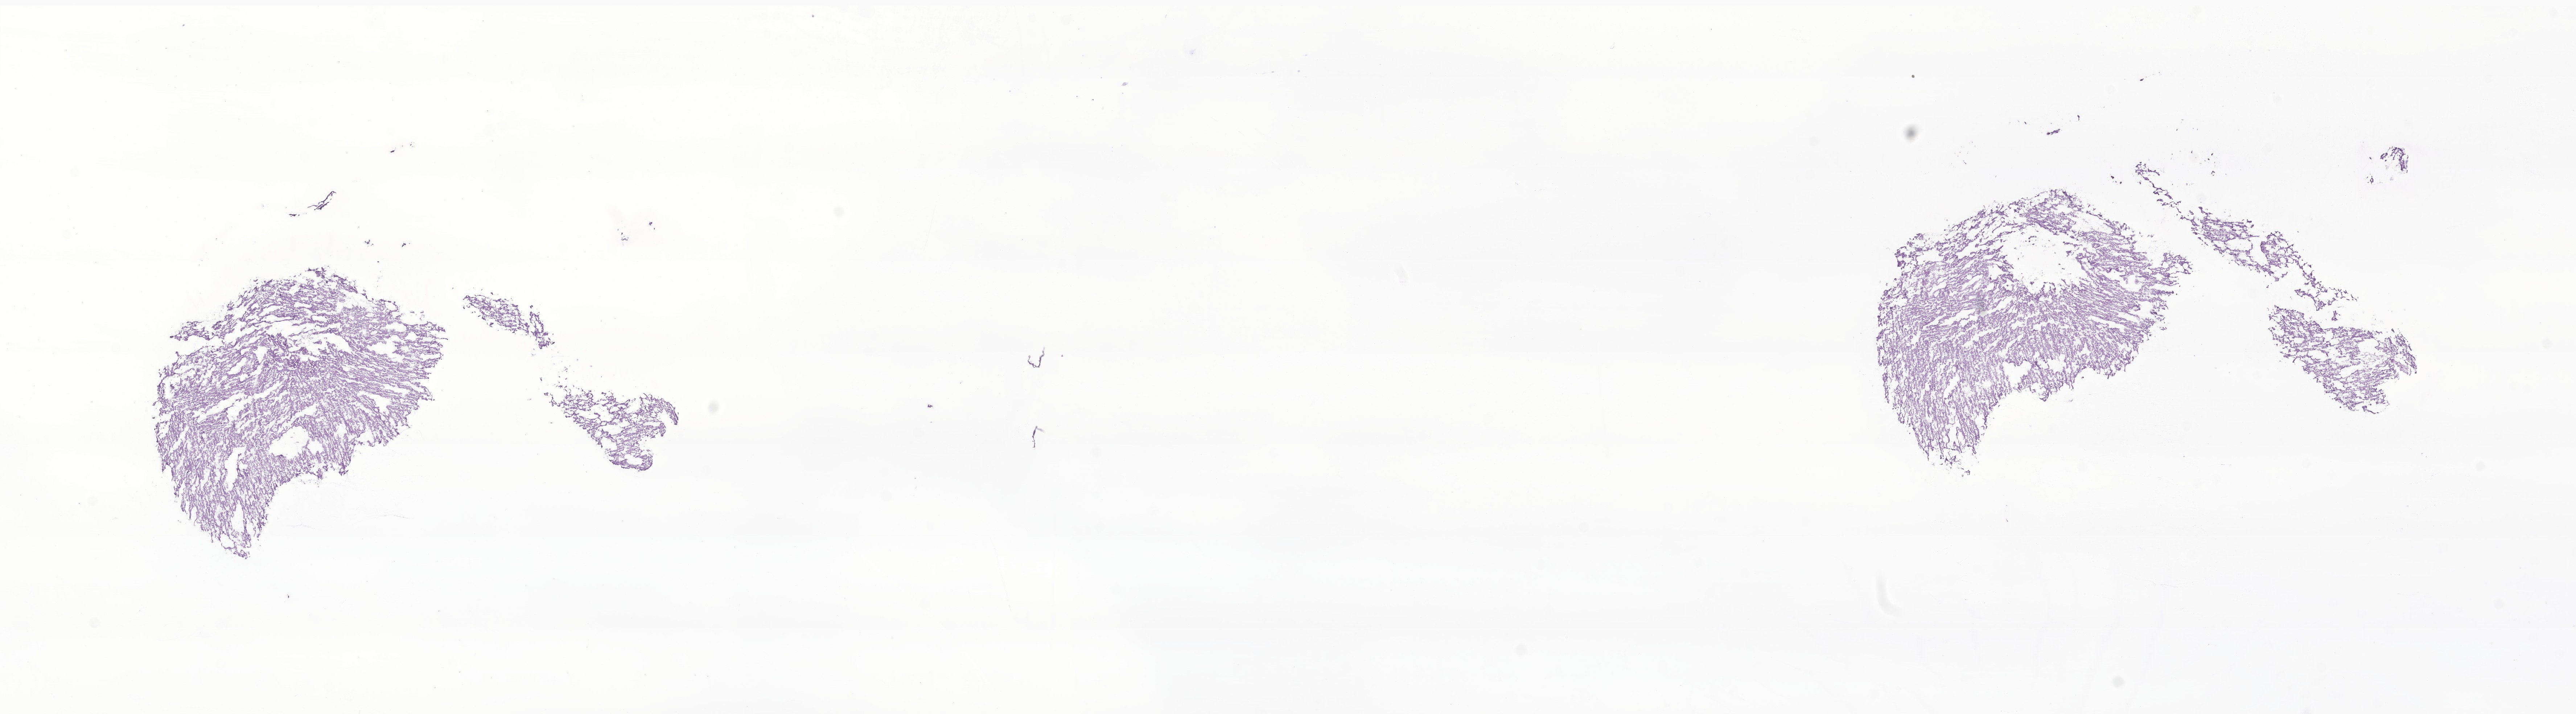
H&E whole-slide image of tumor tissue from the brain, low-resolution overview of the scanned area, about 29.9 x 8.3 mm; cryosection (OCT / tissue freezing medium). Female patient, age 493 days (about 1.3 years).
Diagnosis: Neoplasm, uncertain whether benign or malignant.